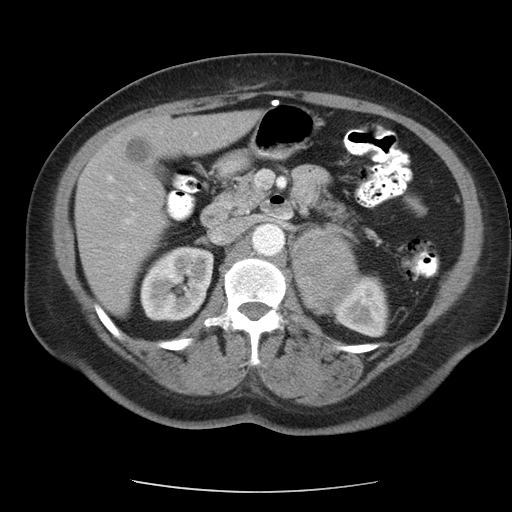
Contrast-enhanced abdominal CT, one axial slice; position 63 of 95 along the scan axis; reconstruction kernel STANDARD; intravenous contrast given; soft-tissue window (W 400 / L 40 HU); 5 mm slice thickness; 512 × 512 image matrix. Female patient, age 71 years. From the clinical record (not read from this slice): diagnosis: adrenocortical carcinoma; tumour side: left adrenal; tumour size at pathology: 8.8 cm; Ki-67 index: 20 %; stage (as recorded): 2.
Annotated regions visible in this slice (semi-automatic segmentation, software-assisted and operator-edited):
- mass: bounding box (x1, y1, x2, y2) in pixels: (292, 233, 356, 310)